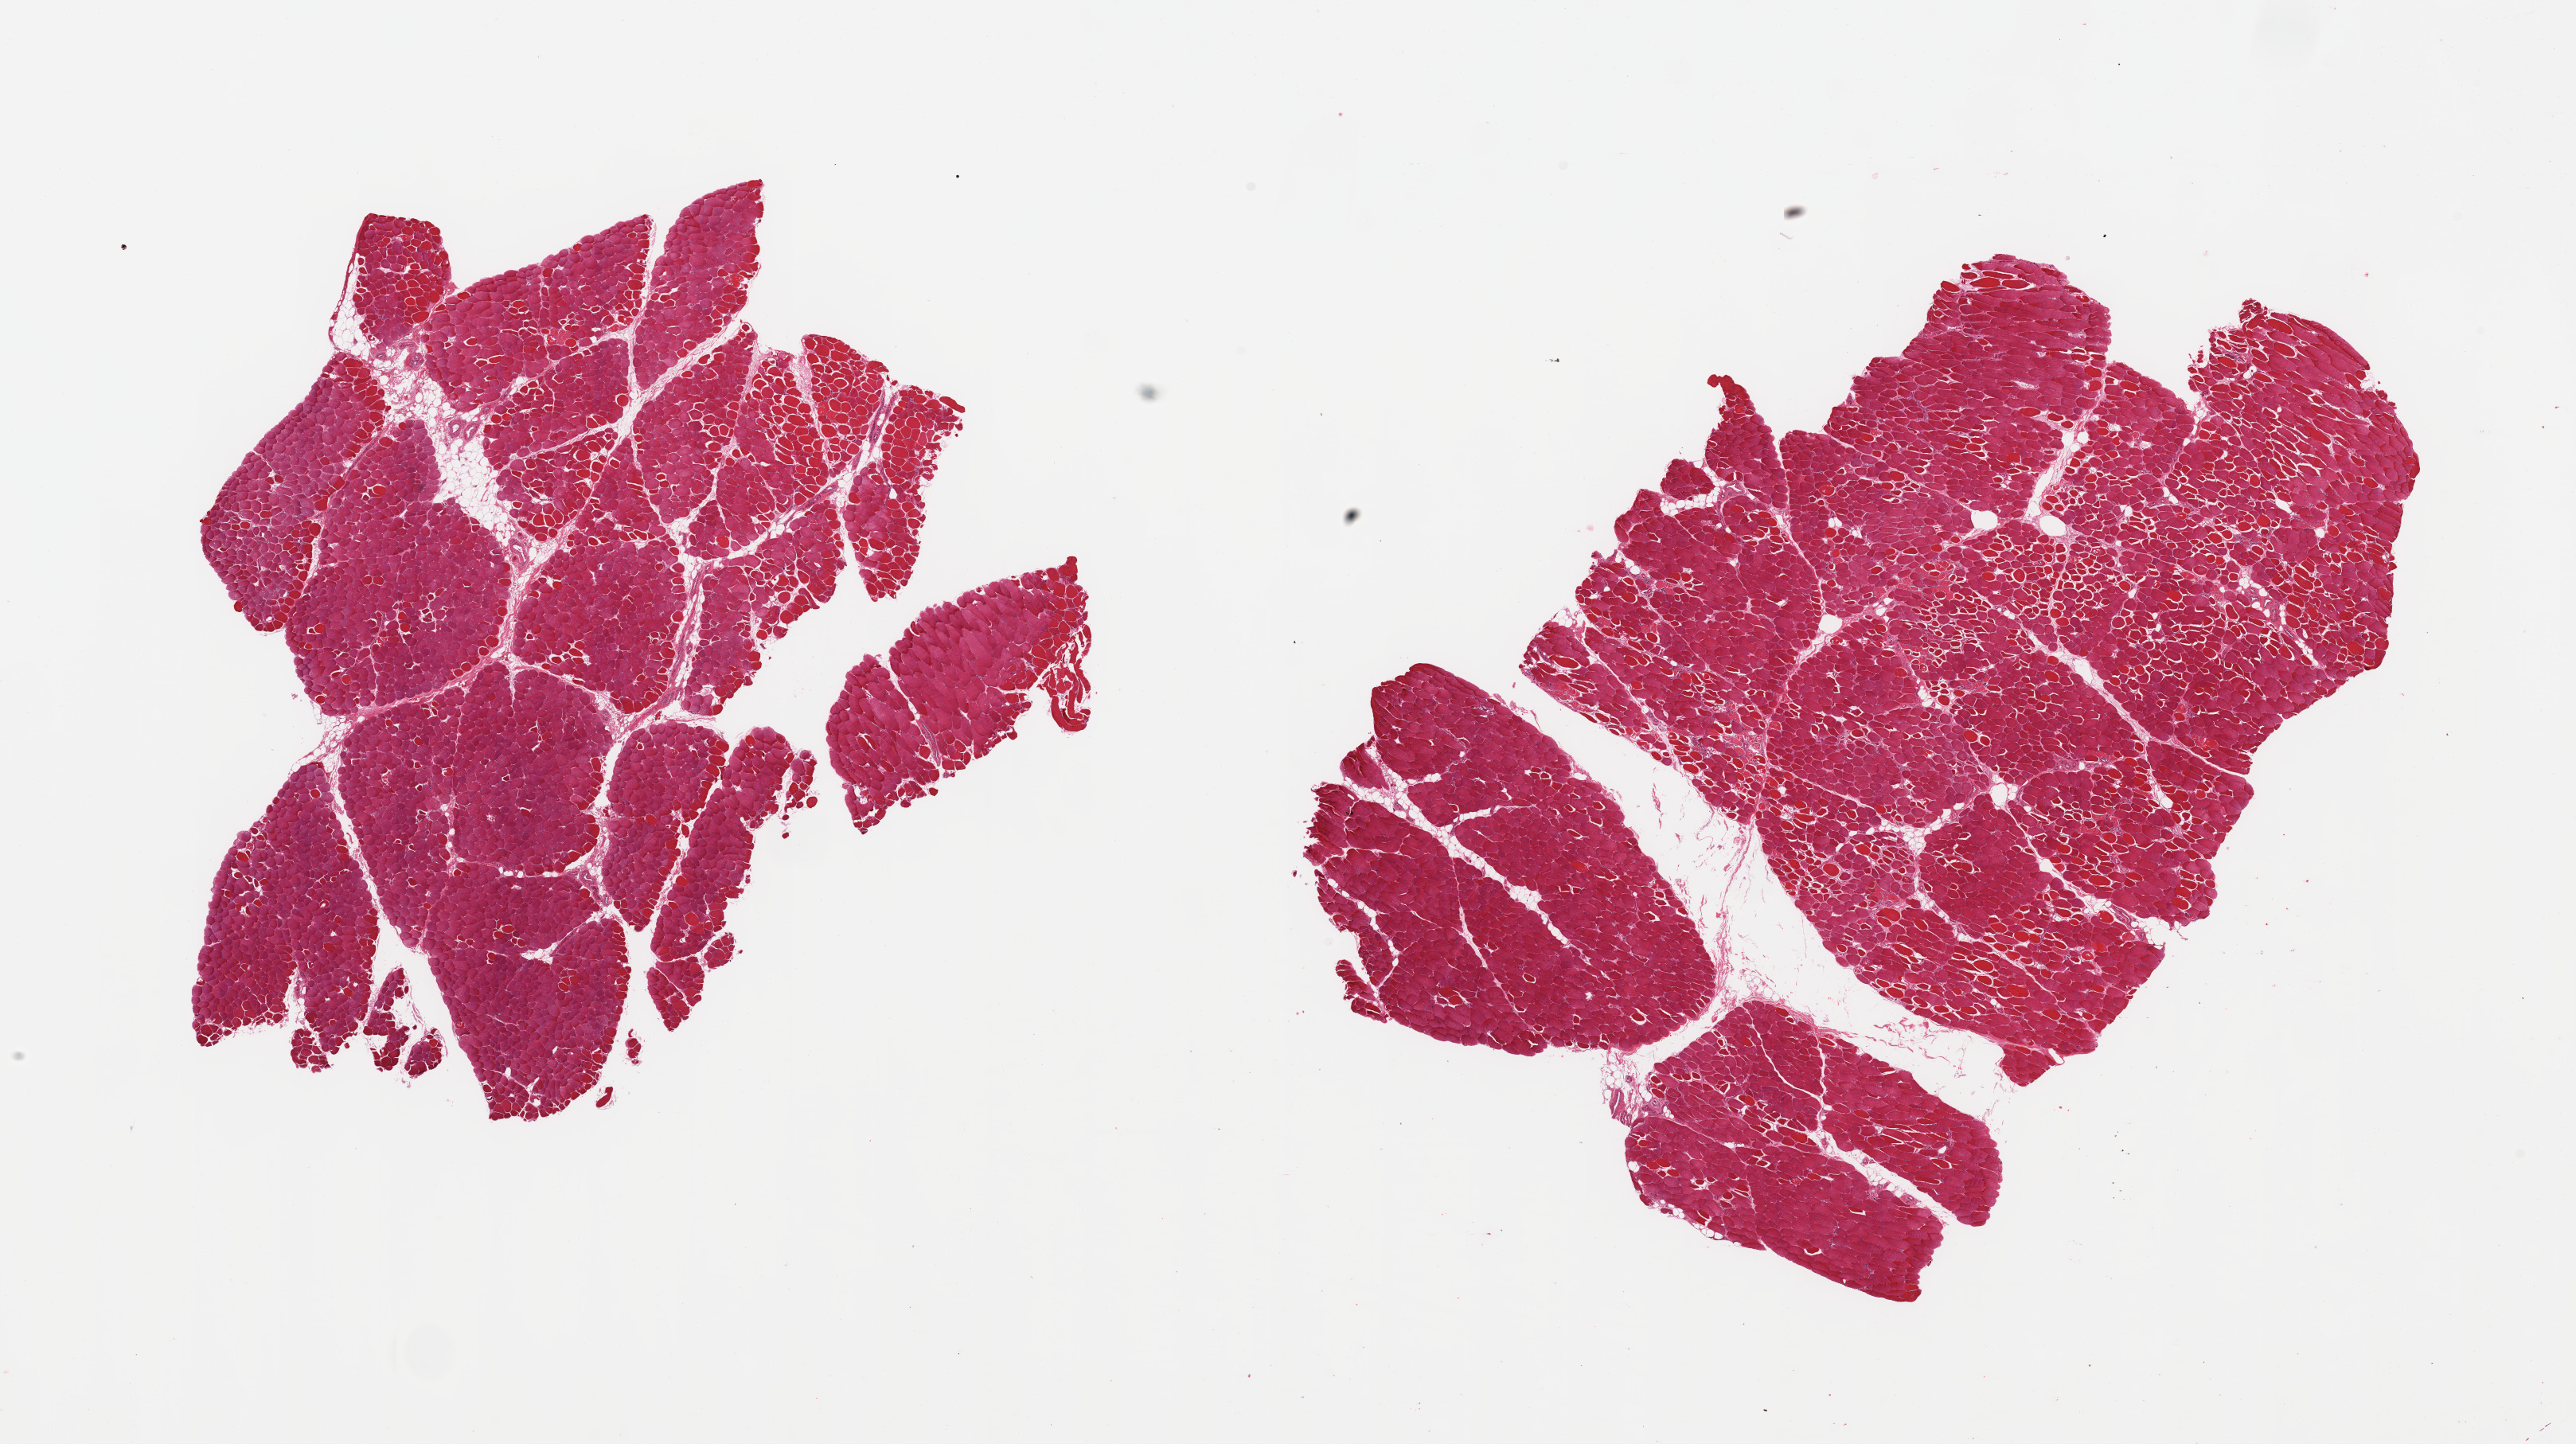
H&E whole-slide image, a low-resolution overview of the entire scanned area, about 25.6 x 14.3 mm; PAXgene-fixed paraffin-embedded (PFPE) section; section of skeletal muscle (target tissue); donor tissue sample. Male donor.
Pathologist's review note for this sample: 2 pieces; <5% fat content.